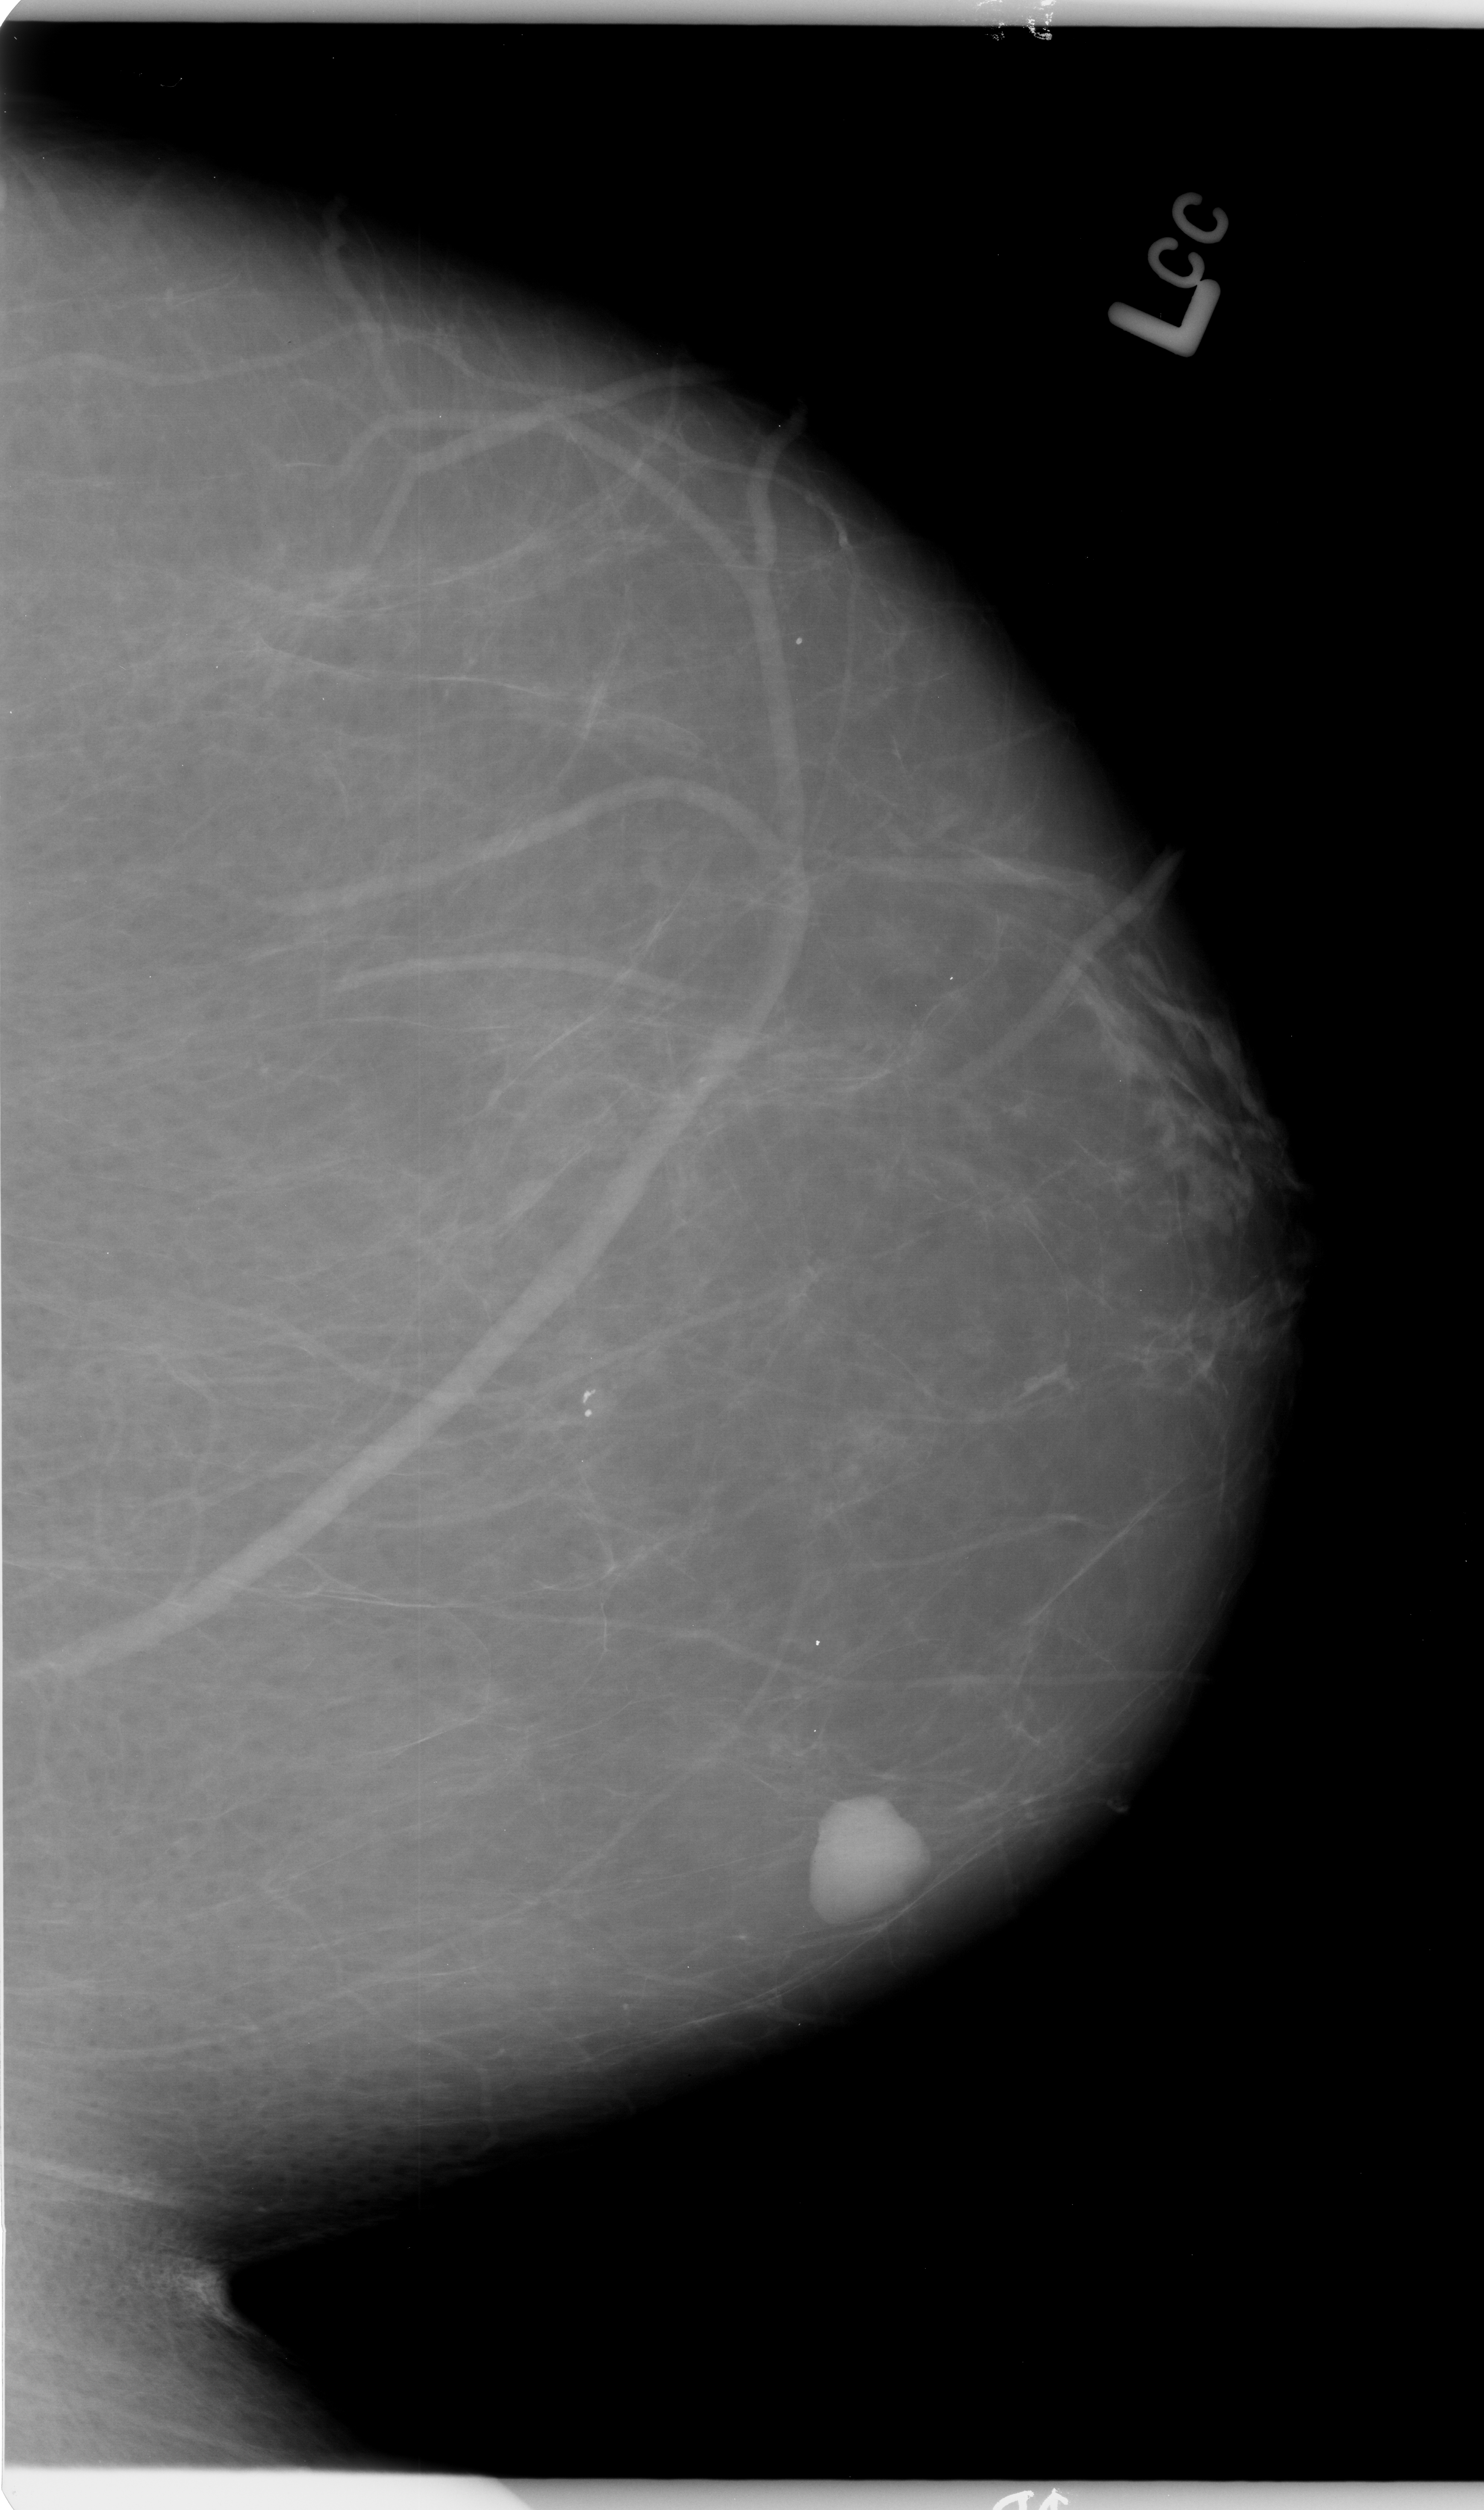
Scanned film-screen mammogram; left breast; CC view; BI-RADS breast density category 1 (scale 1–4); 1484 × 2510 image matrix.
Marked abnormalities (boxes around the expert regions of interest):
- mass, shape oval, margins circumscribed; BI-RADS assessment category 4; pathology result (as recorded, not read from the image): benign: bounding box [x1, y1, x2, y2] px = [809, 1794, 919, 1914]